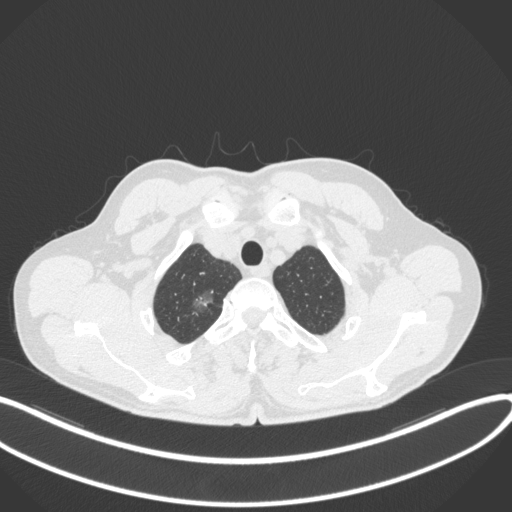
Chest CT, one axial slice; position 342 of 407 along the scan axis; 120 kVp; lung window (W 1500 / L -600 HU); 512 × 512 image matrix, field of view 400 × 400 mm. Patient: male, 58 years. Case-level facts recorded for this patient, not image findings: clinical TNM (as recorded): T1c N0 M0.
Annotated regions visible in this slice (rectangle marked by the reading radiologist):
- lung tumour (recorded histology: adenocarcinoma): bounding box [x1, y1, x2, y2] px = [183, 286, 219, 316]